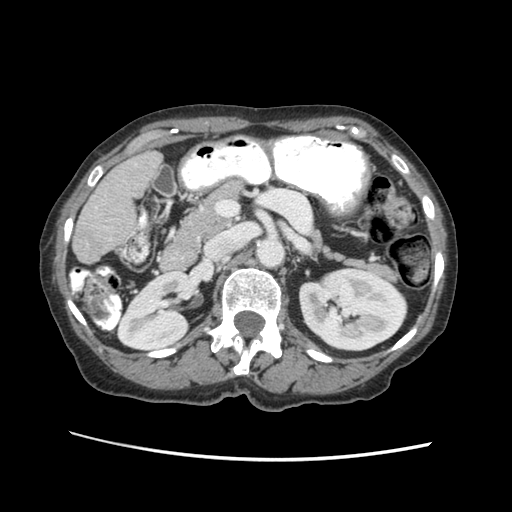
Contrast-enhanced abdominal CT (liver protocol), one axial slice; position 17 of 63 along the scan axis; reconstruction kernel STANDARD; soft-tissue window (W 400 / L 40 HU); 2.5 mm slice thickness; 512 × 512 image matrix, field of view 340 × 340 mm. Case-level facts recorded for this patient, not image findings: diagnosis: hepatocellular carcinoma (patient treated with transarterial chemoembolisation; whether this scan precedes or follows treatment is not stated here); TNM stage (as recorded): Stage-I; Child-Pugh class: B; tumour differentiation: well differentiated; tumour nodularity: uninodular.
Structures marked on this image (semi-automatically segmented with operator editing):
- liver parenchyma outside the tumour (the mass and vessels are separate outlines, so this box may not span the whole liver): bounding box [x1, y1, x2, y2] px = [72, 150, 160, 262]